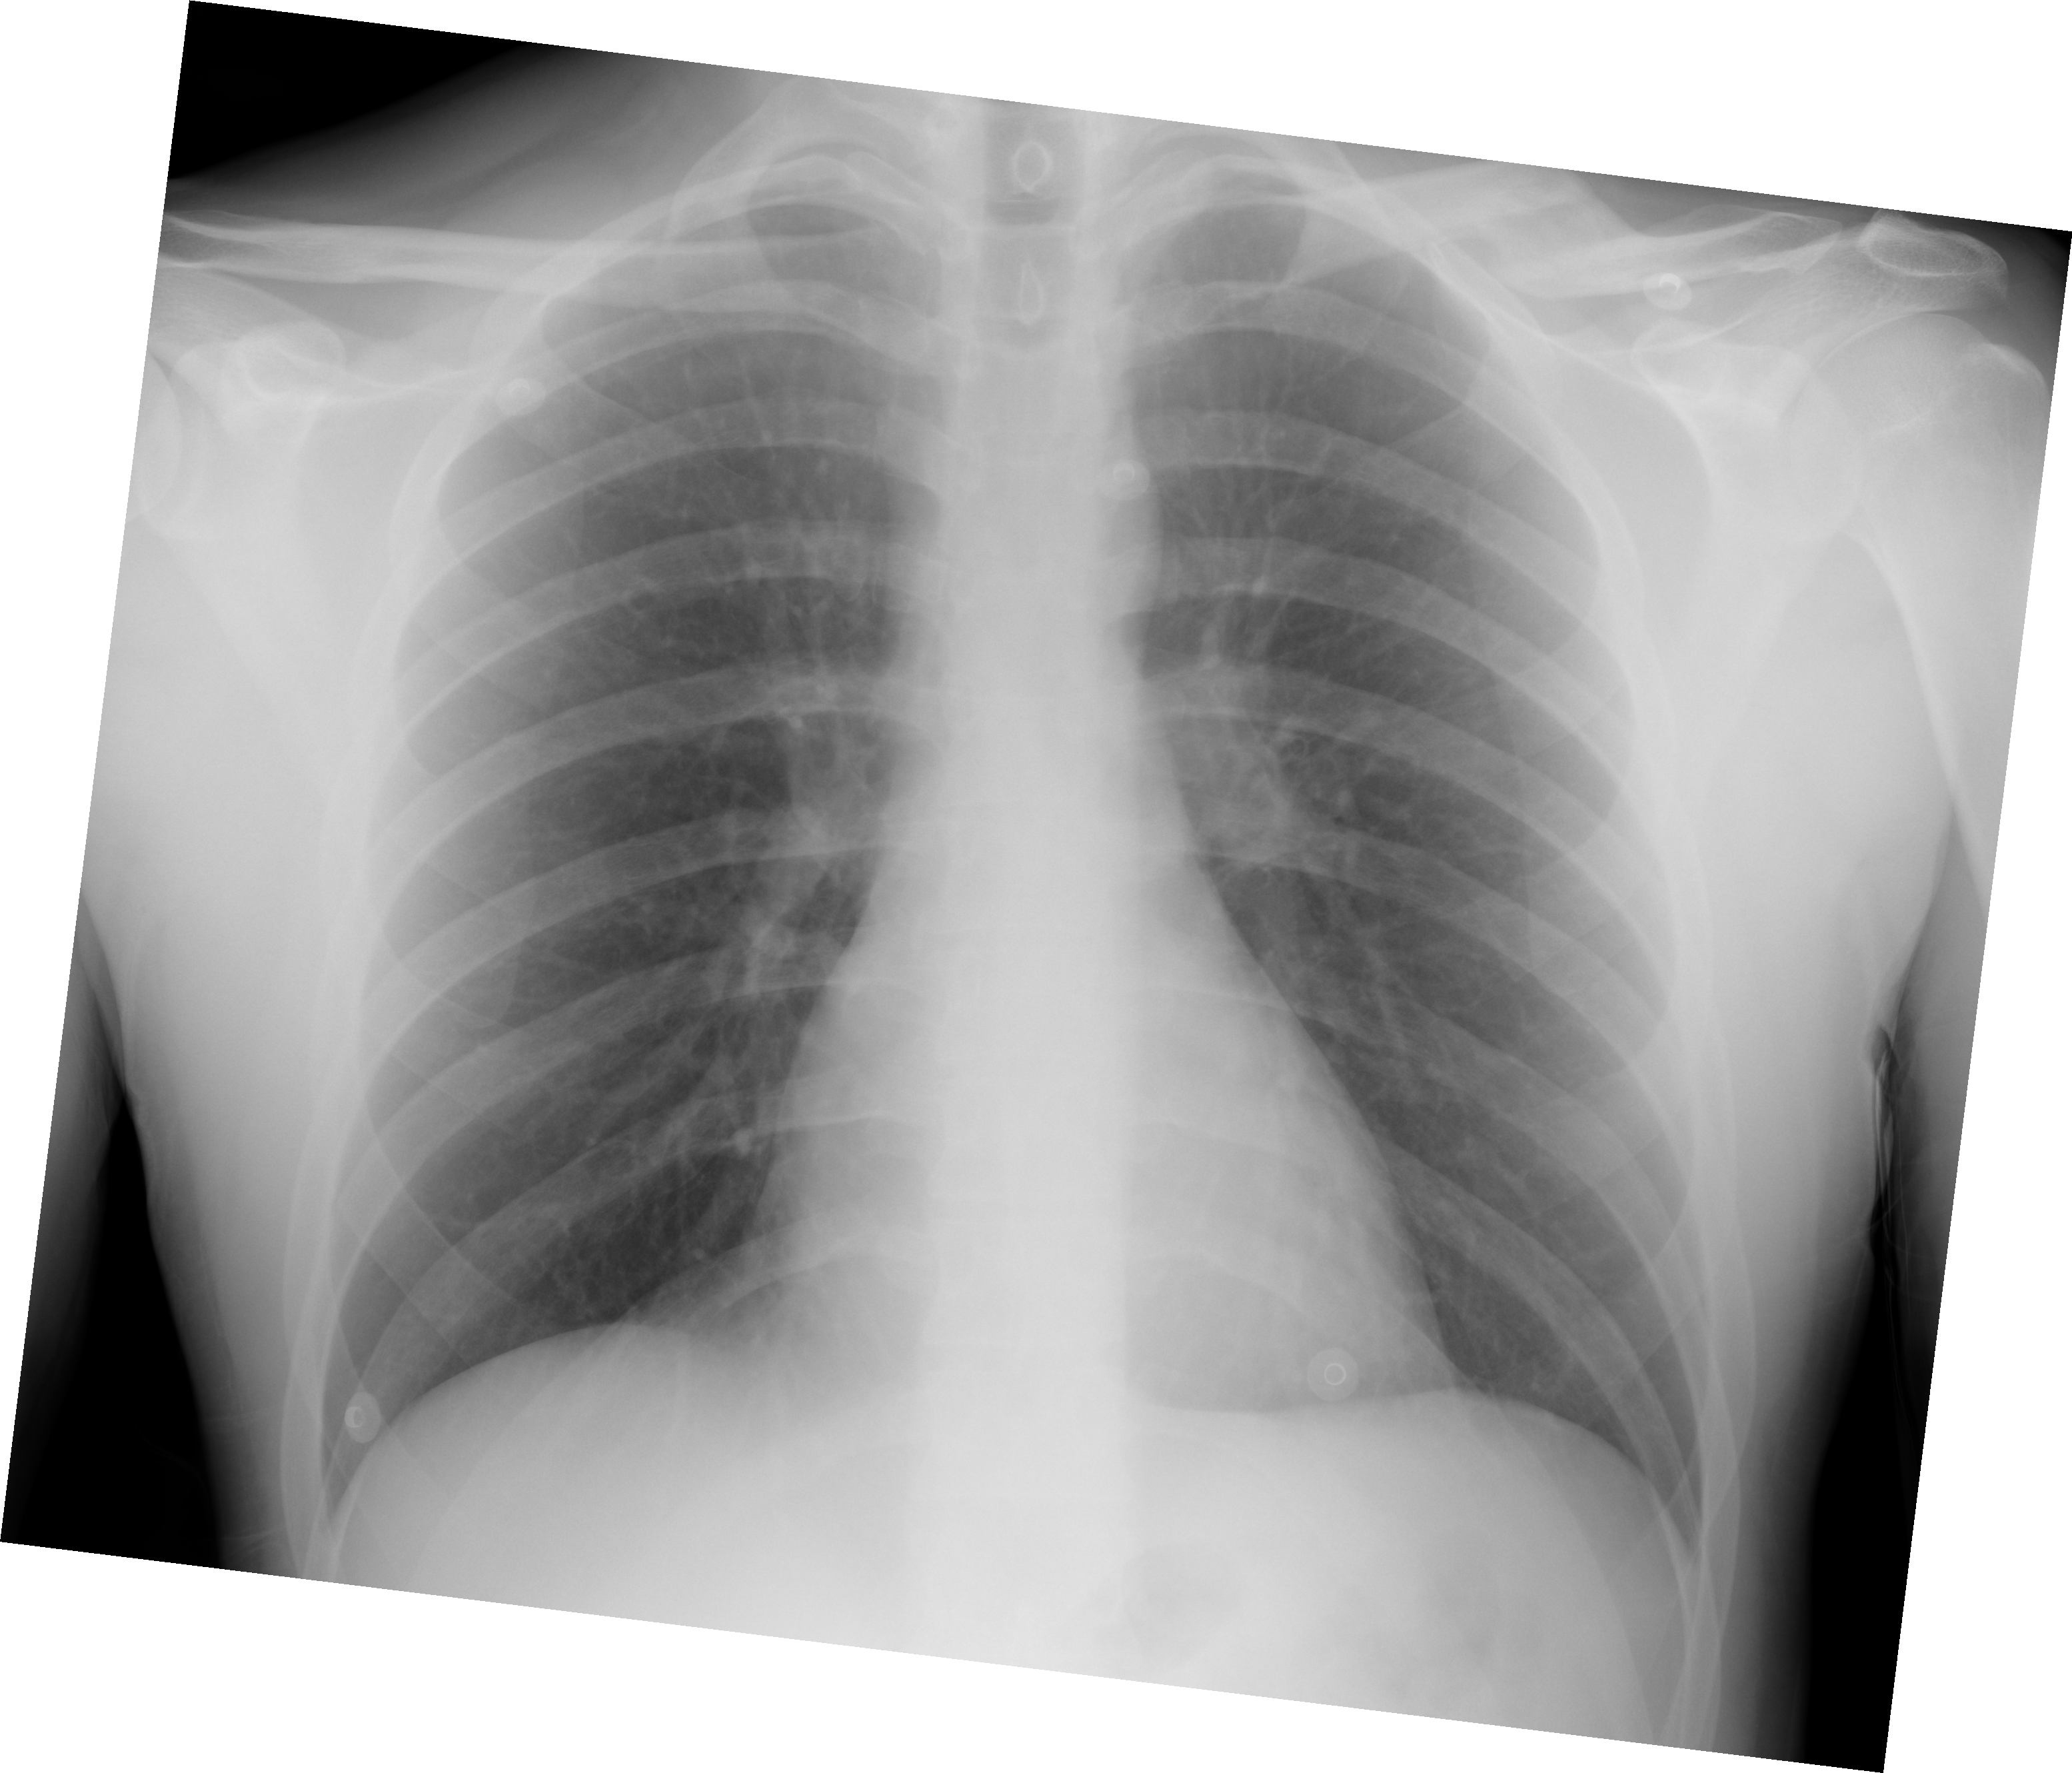
Portable chest radiograph, AP projection. Male patient, age 26 years; imaged 0 days after the COVID-19 diagnosis.
Radiologist's key findings for this exam: he lungs are clear without focal airspace opacification.